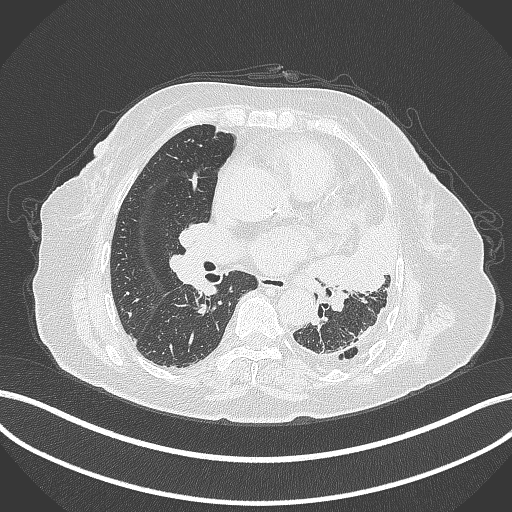
Chest CT, one axial slice. Position 188 of 399 along the scan axis. Reconstruction kernel B70f. Lung window (W 1500 / L -600 HU). 1 mm slice thickness. 512 × 512 image matrix. Patient: female, 75 years. Case-level facts recorded for this patient, not image findings: clinical TNM (as recorded): T3 N3 M1.
Outlined on this slice (rectangle marked by the reading radiologist):
- lung tumour (recorded histology: adenocarcinoma): bounding box (x1, y1, x2, y2) in pixels: (305, 219, 395, 303)